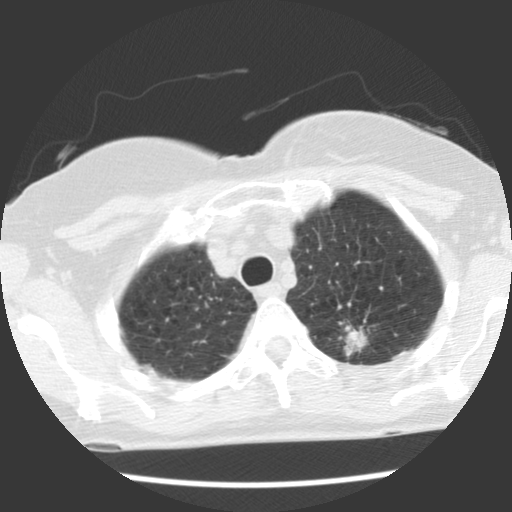
Axial slice from a low-dose chest CT screening exam. First (baseline) screen. Lung window (W 1500 / L -600 HU). 2.5 mm slice thickness. Standard (soft-tissue) reconstruction kernel (STANDARD). Slice 97 of 120 in the series. Female participant, aged 66 years at enrolment.
• Expert reader's lesion annotation, bounding box (x1, y1, x2, y2) in pixels: (319, 309, 389, 374).
• Screening reader's record for this exam (one nodule recorded; not confirmed to be the boxed lesion): non-calcified nodule or mass ≥4 mm, left upper lobe, 22 × 17 mm, spiculated (stellate) margins, soft tissue attenuation.
• Official screen result: positive, change unspecified: nodule(s) >= 4 mm or enlarging nodule(s), mass(es), or other non-specific abnormalities suspicious for lung cancer.
• Later outcome: lung cancer diagnosed 50 days after this screen — adenocarcinoma, NOS, left upper lobe, poorly differentiated (G3), stage IB (AJCC 6th edition), 40 mm at pathology.